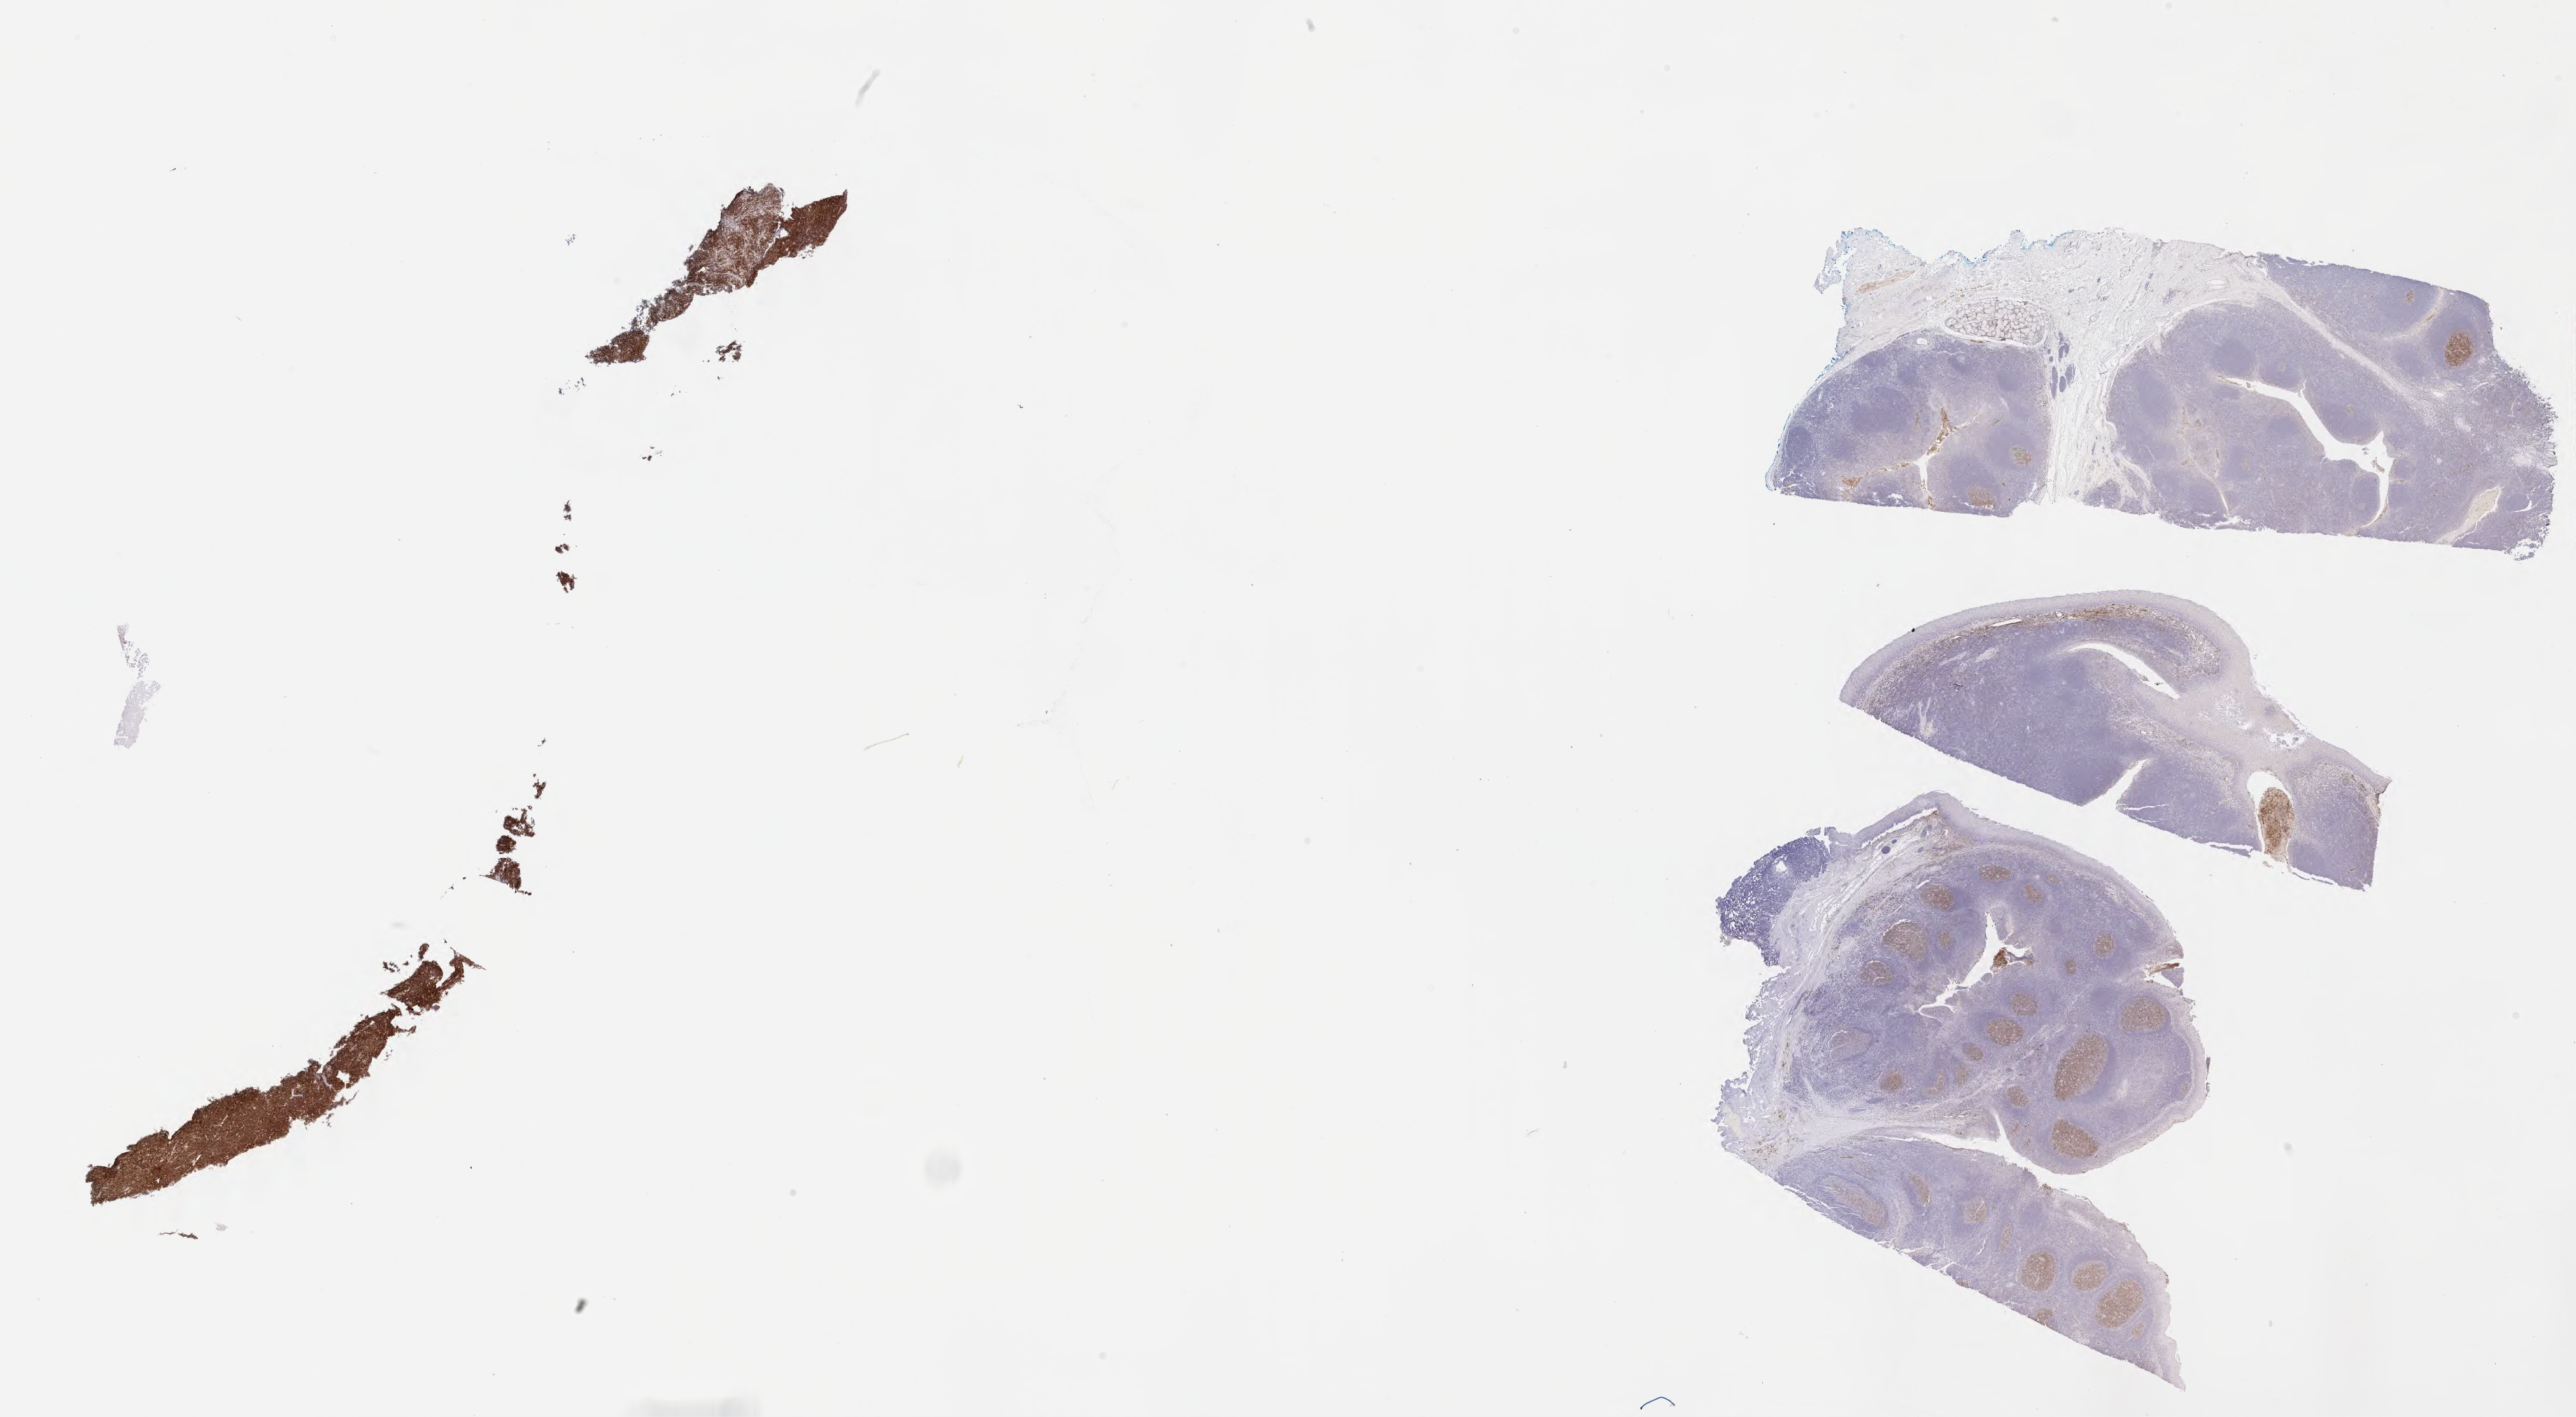
Immunohistochemistry (IHC) whole-slide image stained for CD10, low-resolution overview of the scanned area, about 32.7 x 18.0 mm; tumor tissue; anatomic site: cranium. Female patient; age at initial diagnosis 7 years.
• histologic diagnosis: Burkitt lymphoma, NOS